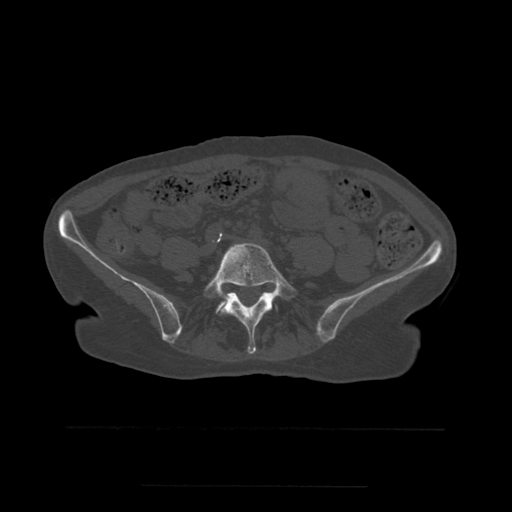
CT including the spine, one axial slice. Slice 145 of 544 in the series (ordered by position). Bone window (W 1800 / L 400 HU). 1.25 mm slice thickness. 512 × 512 image matrix, field of view 350 × 350 mm. Patient age 58 years. Case-level facts recorded for this patient, not image findings: primary cancer: lung.
Annotated regions visible in this slice (semi-automatically segmented with operator editing):
- L5 vertebra: box from (x=204, y=243) to (x=297, y=354) px